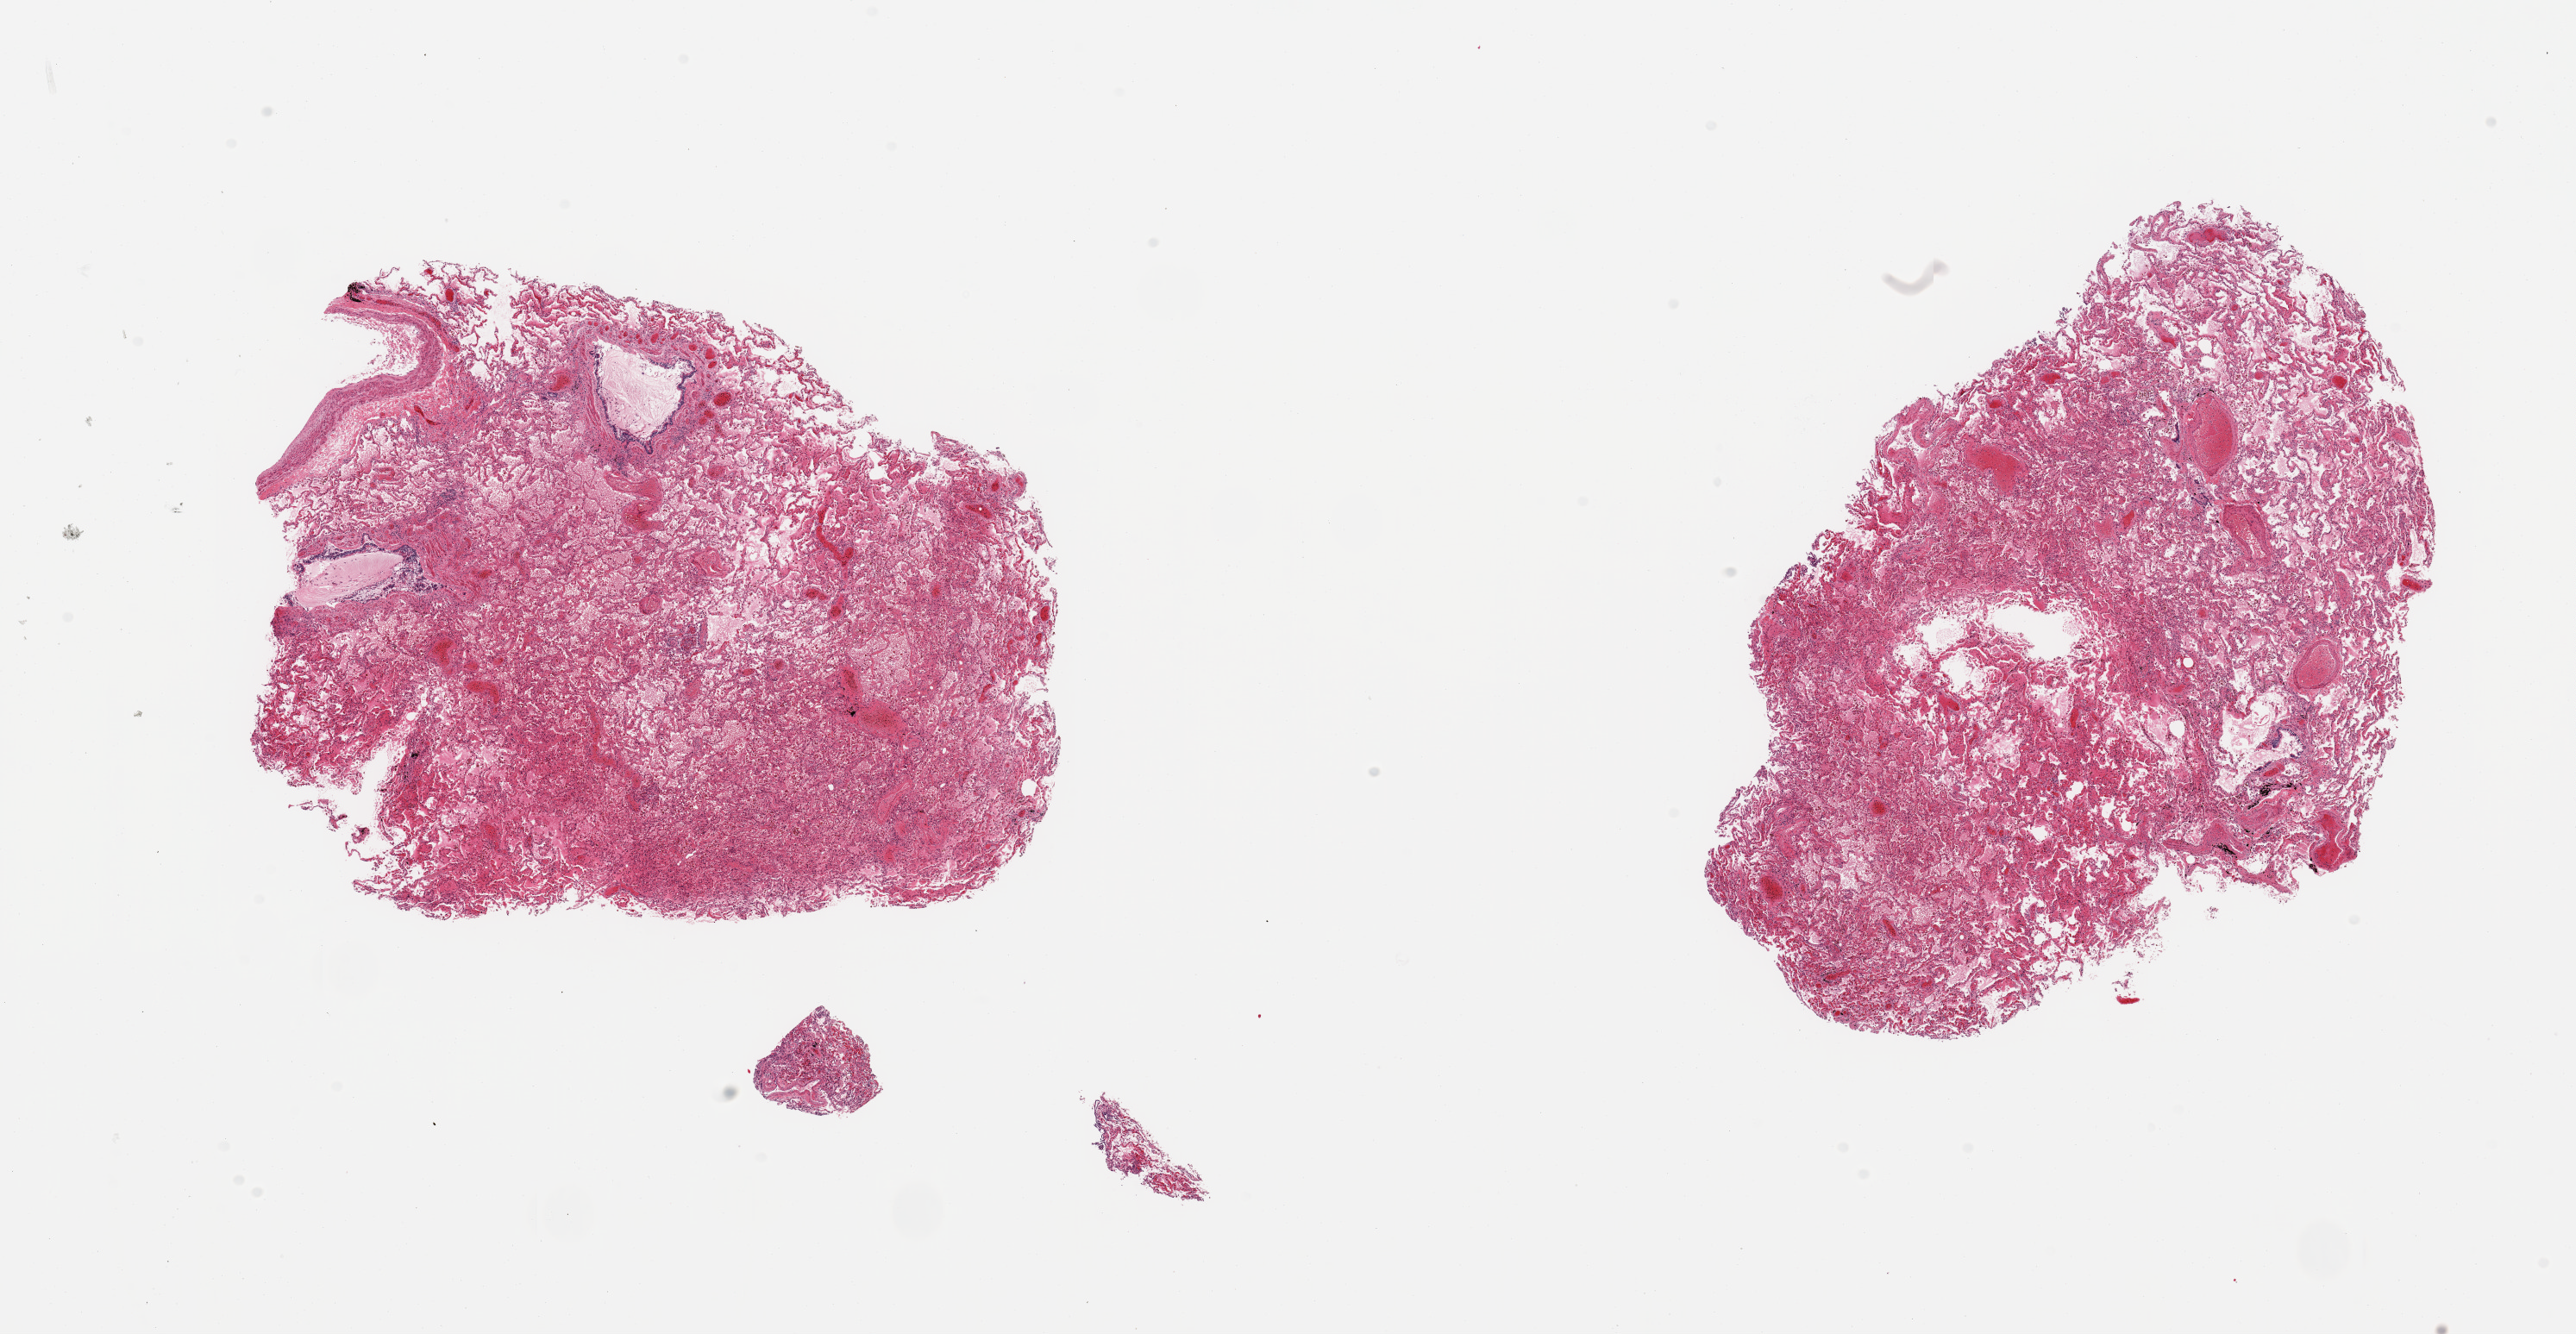
Whole-slide image, H&E stain, low-resolution overview of the scanned area, about 23.6 x 12.2 mm (slide scanned at 20x), PAXgene-fixed, paraffin-embedded tissue, target tissue: lung, tissue donor sample. Donor sex: male.
Pathologist's review note for this sample: 2 pieces, moderate-severe alveolar edema/congestion.